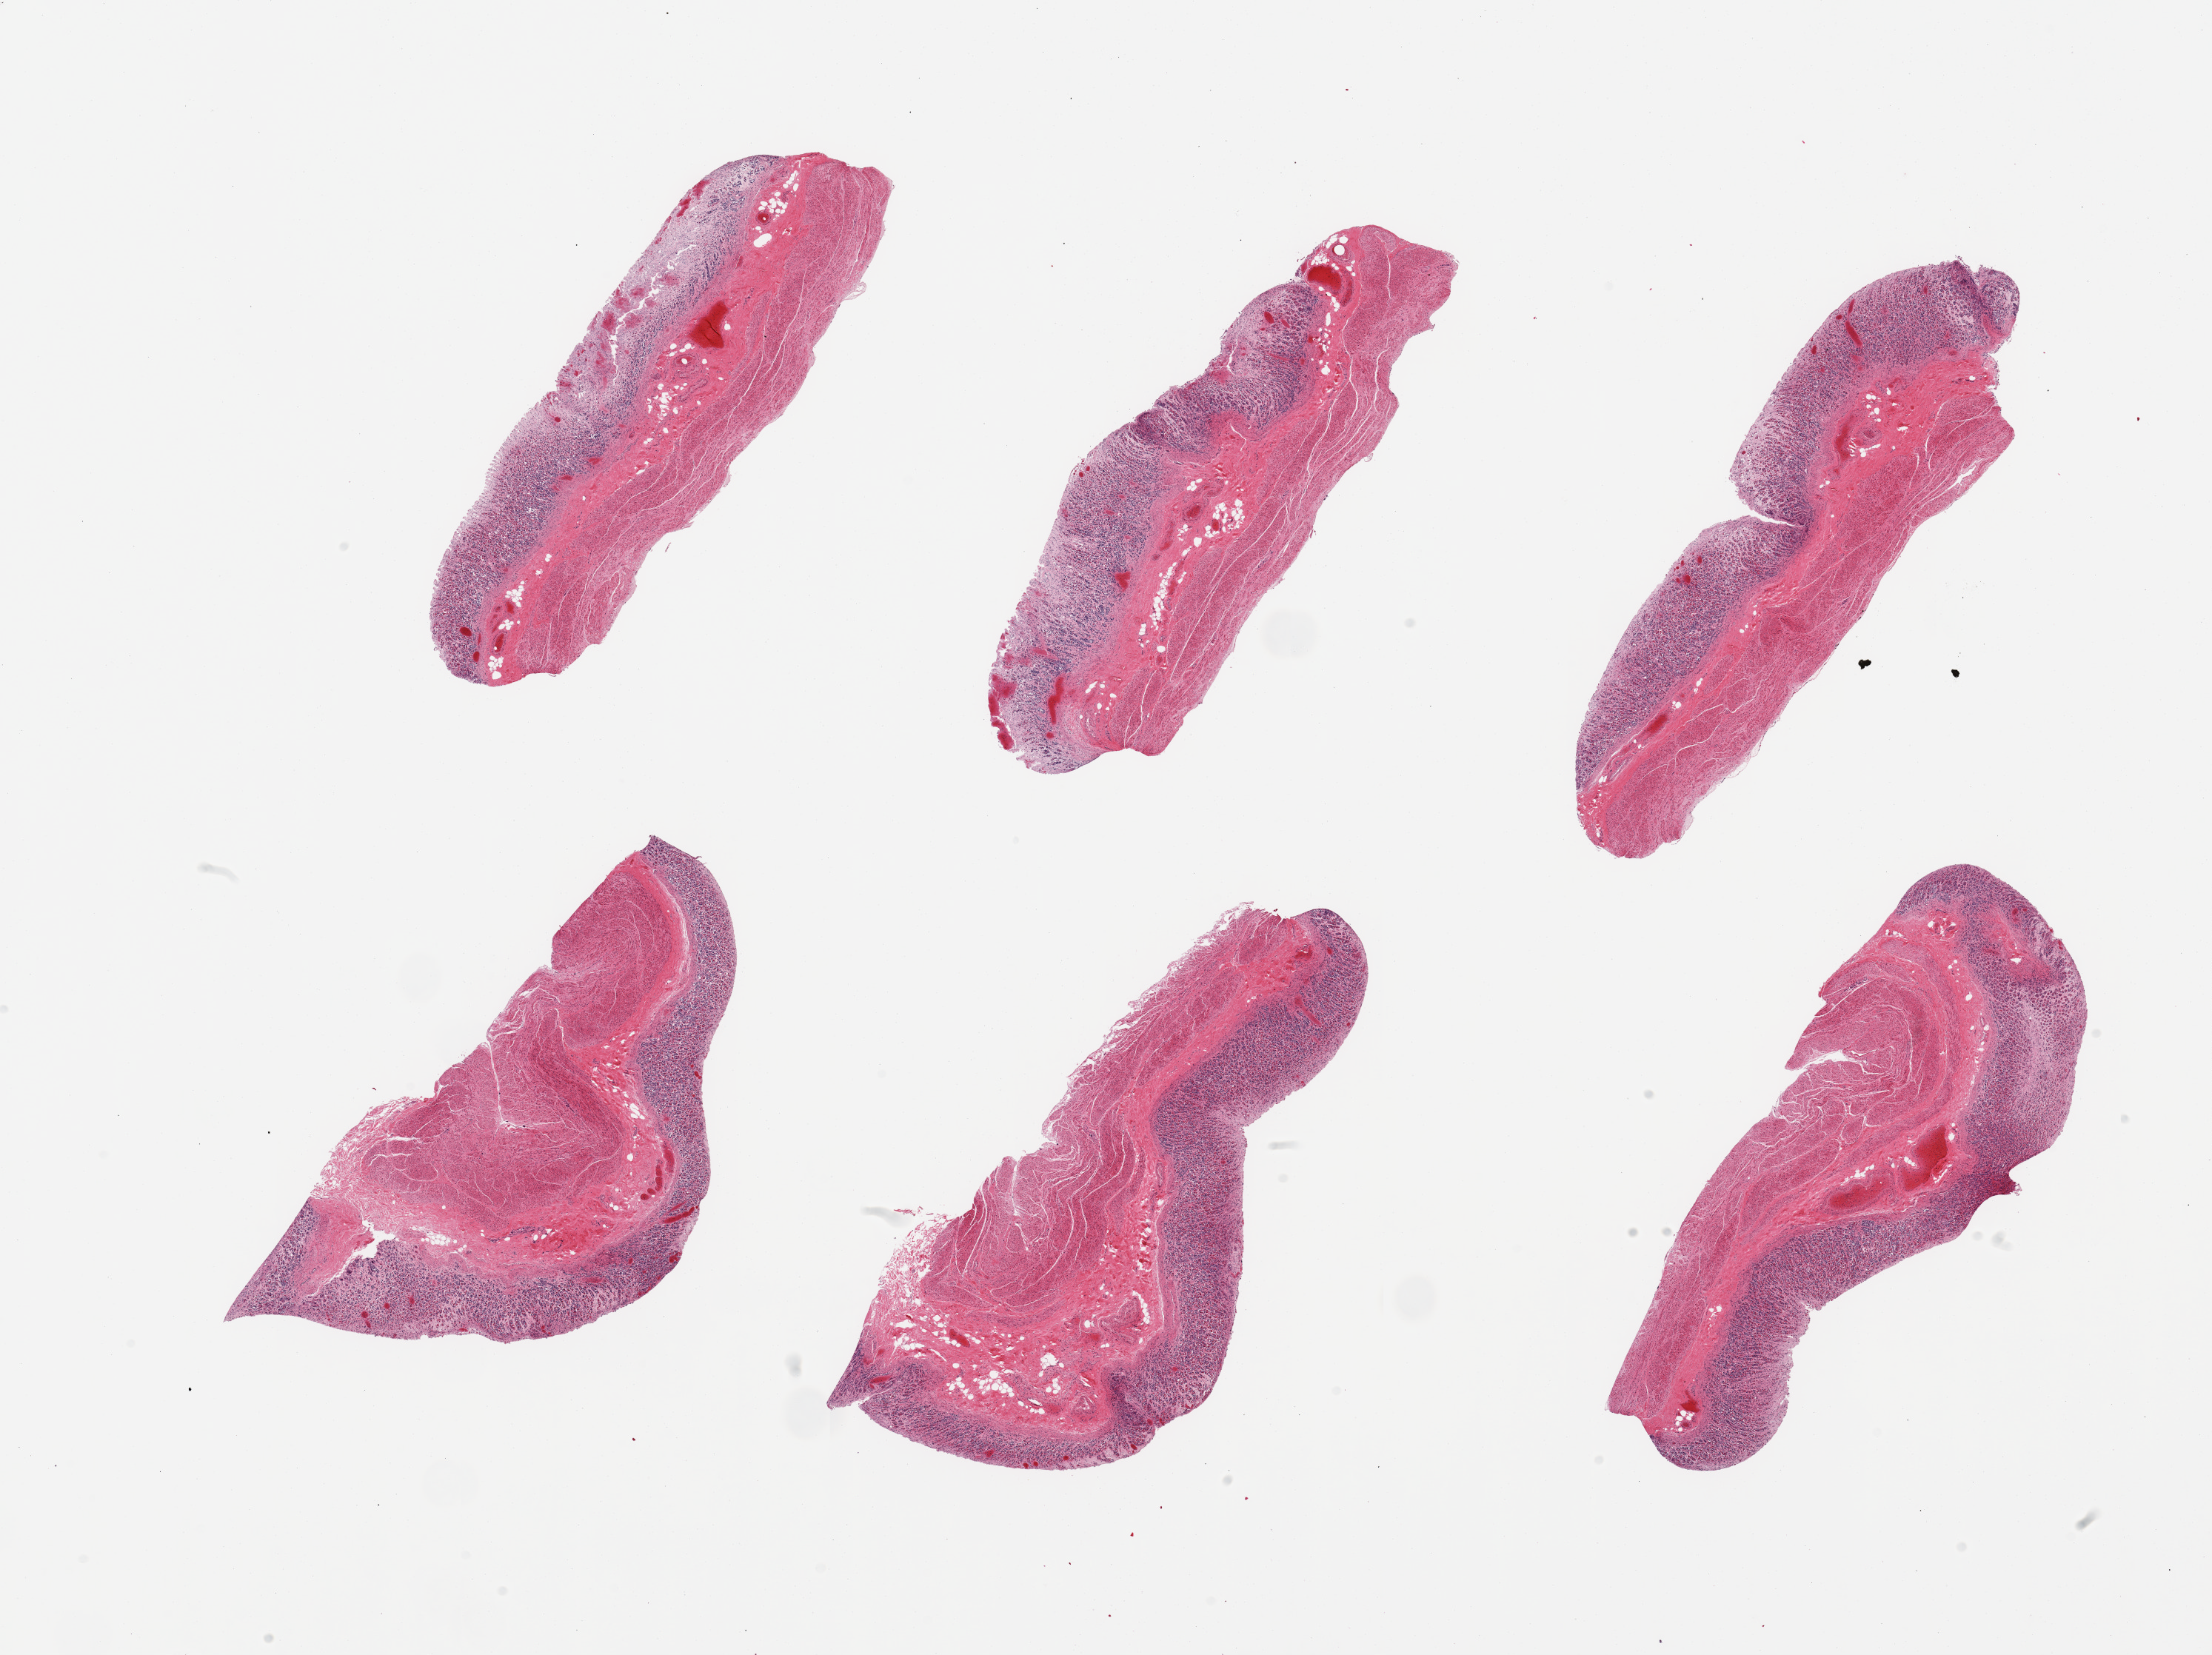
Digitized hematoxylin and eosin (H&E)-stained section — shown as a low-resolution overview of the whole scanned area (about 23.6 x 17.7 mm, from a 20x scan), PAXgene-fixed paraffin-embedded (PFPE) section, target tissue: stomach, tissue donor sample. Donor sex: female.
Pathologist's review note for this sample: 6 pieces; mucosa =3; muscle =2 autolysis.